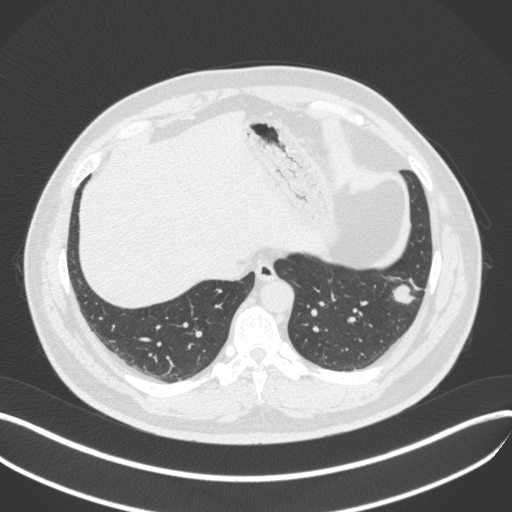
Chest CT, one axial slice; slice 111 of 420 in the series (ordered by position); reconstruction kernel B31f; lung window (W 1500 / L -600 HU); 1 mm slice thickness; 512 × 512 image matrix. Male patient, age 39 years. From the clinical record (not read from this slice): clinical TNM (as recorded): T2a N0 M0; histopathological grade: G2-3.
Outlined on this slice (rectangle marked by the reading radiologist):
- lung tumour (recorded histology: adenocarcinoma): bounding box [x1, y1, x2, y2] px = [387, 274, 422, 309]